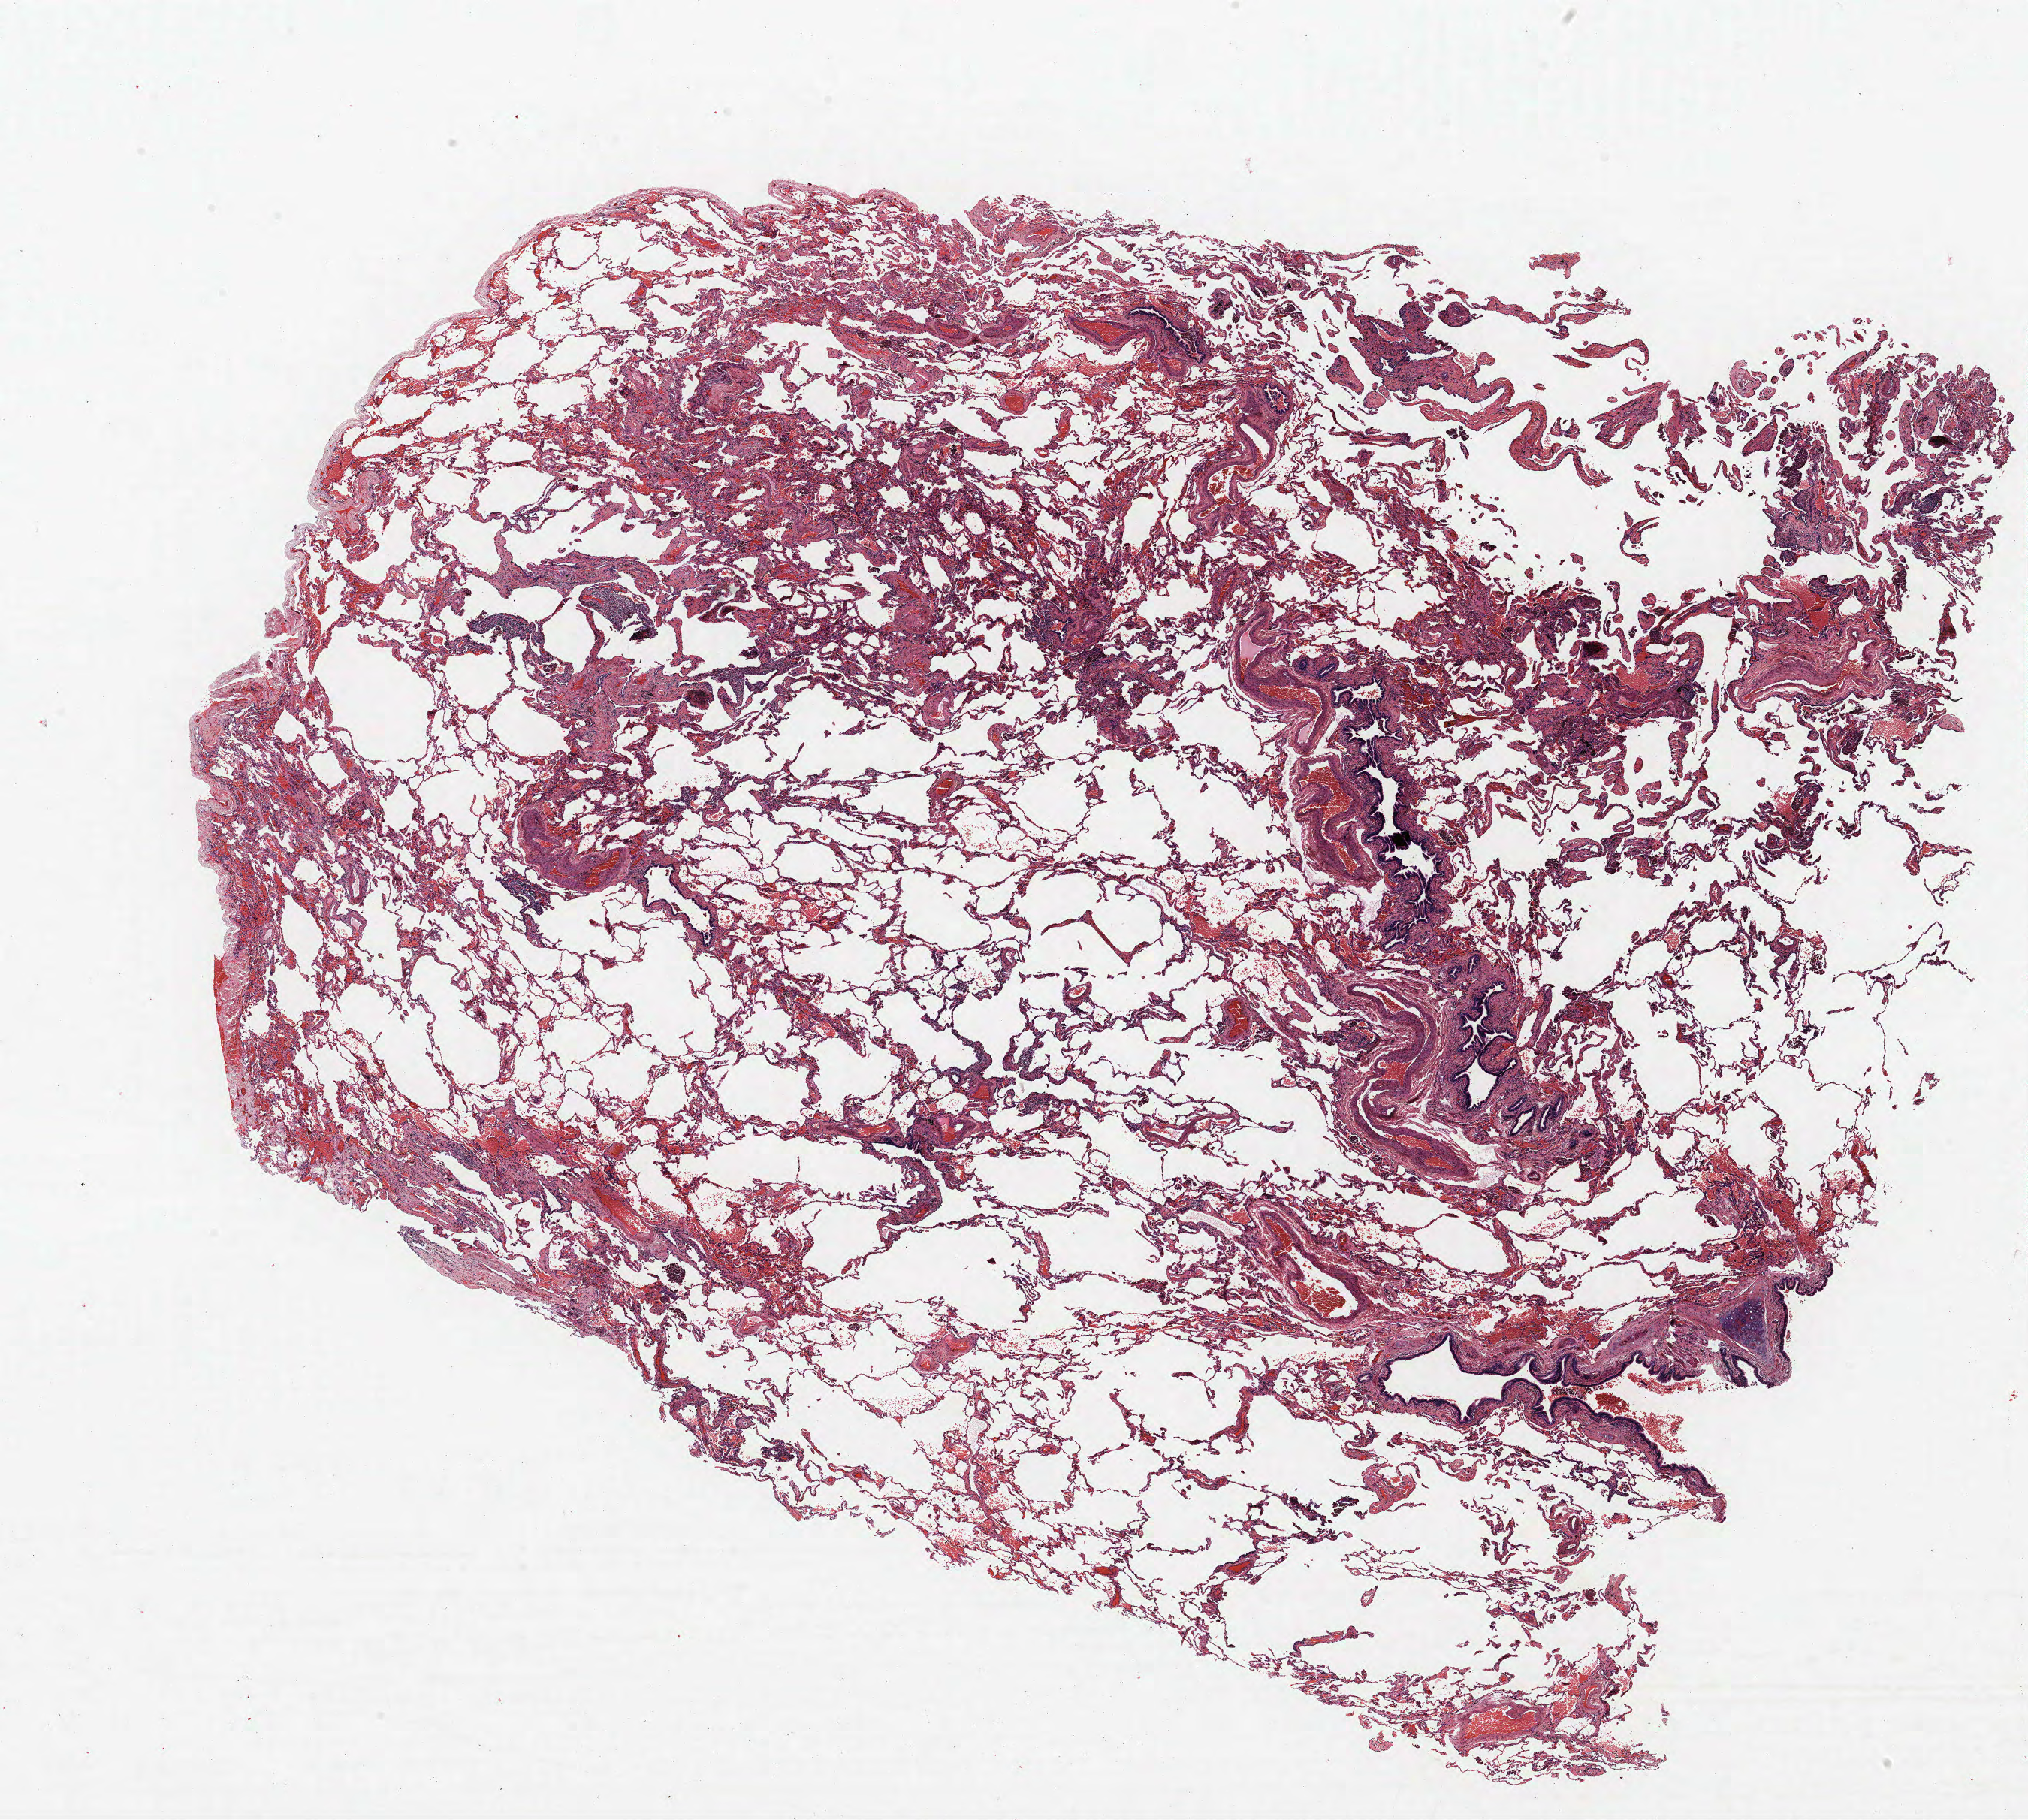
Hematoxylin and eosin (H&E) stained whole-slide image, whole scanned area (about 21.6 x 19.4 mm) shown as a low-resolution overview; FFPE section; lung. Female patient, aged 56 at enrolment. Grade: poorly differentiated (G3).
• participant's lung-cancer diagnosis: Adenocarcinoma, NOS
• ICD-O-3 topography: upper lobe of lung (C34.1)
• tumour size (pathology): 20 mm
• stage (AJCC 6th edition): IIA
• primary tumour location (clinical record): right upper lobe